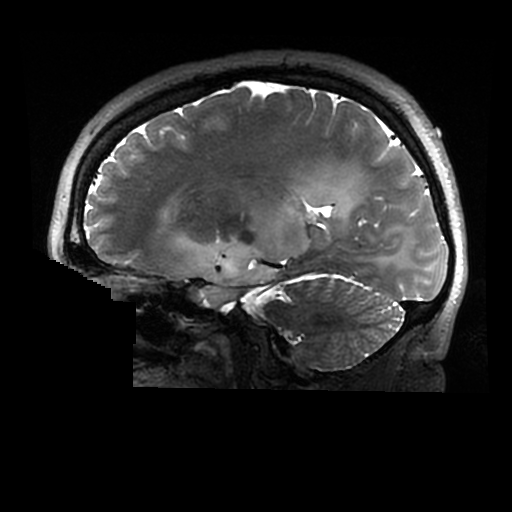
Brain MRI from a brain-tumour surgery series, one sagittal slice; position 181 of 320 along the scan axis; 512 × 512 image matrix, field of view 240 × 240 mm. From the clinical record (not read from this slice): histopathology: Astrocytoma; WHO grade: 2; IDH mutation: yes.
Structures marked on this image (expert manual segmentation):
- tumour: bounding box [x1, y1, x2, y2] px = [177, 186, 355, 309]